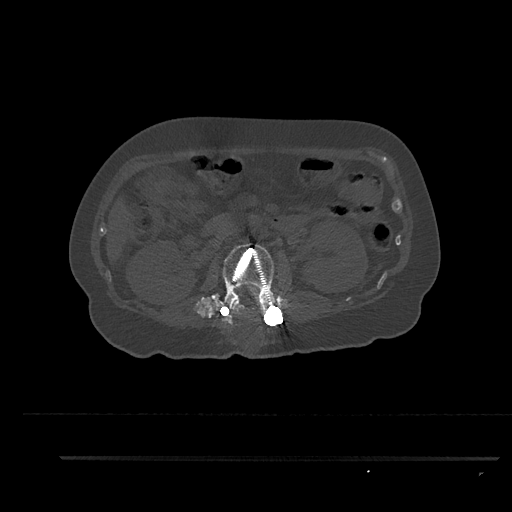
CT including the spine, one axial slice; reconstruction kernel Br40s/3; bone window (W 1800 / L 400 HU); 0.5 mm slice thickness; 512 × 512 image matrix. Patient: female, 44 years. Case-level facts recorded for this patient, not image findings: primary cancer: renal; vertebrae with lytic lesions (as recorded): L1.
Outlined on this slice (semi-automatic segmentation, software-assisted and operator-edited):
- L2 vertebra: bounding box [x1, y1, x2, y2] px = [214, 243, 276, 320]